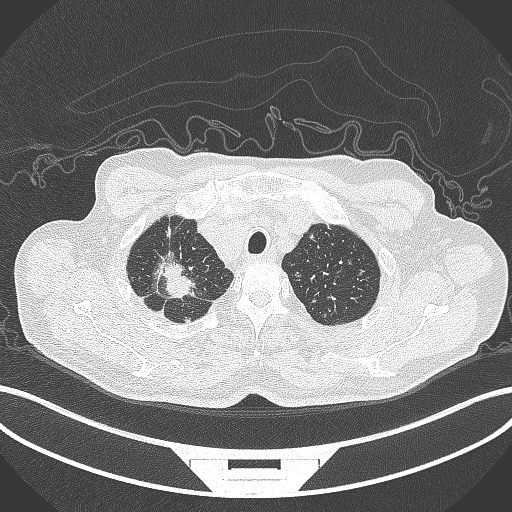
Chest CT, one axial slice; slice 337 of 407 in the series (ordered by position); lung window (W 1500 / L -600 HU); 1 mm slice thickness; 512 × 512 image matrix, field of view 400 × 400 mm. Male patient, age 69 years. From the clinical record (not read from this slice): clinical TNM (as recorded): T1c N1 M1.
Annotated regions visible in this slice (rectangle marked by the reading radiologist):
- lung tumour (recorded histology: adenocarcinoma): bounding box <145,246,203,303> (left, top, right, bottom; pixels)